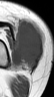
MRI of an extremity soft-tissue mass, one axial slice; slice 23 of 42 in the series (ordered by position); MR volume resampled by the dataset authors to the PET/CT grid (not the native acquisition matrix); 3.27 mm slice thickness; 54 × 97 image matrix. Female patient. From the clinical record (not read from this slice): histological type: spindle cell suggestive of biphasic synovial sarcoma; grade: intermediate; site of the primary tumour: left knee.
Outlined on this slice (expert contour drawn on MRI and transferred to this co-registered scan by the dataset authors):
- gross tumour volume including surrounding oedema: bounding box <12,19,43,70> (left, top, right, bottom; pixels)
- gross tumour volume (mass): <14,21,43,70>